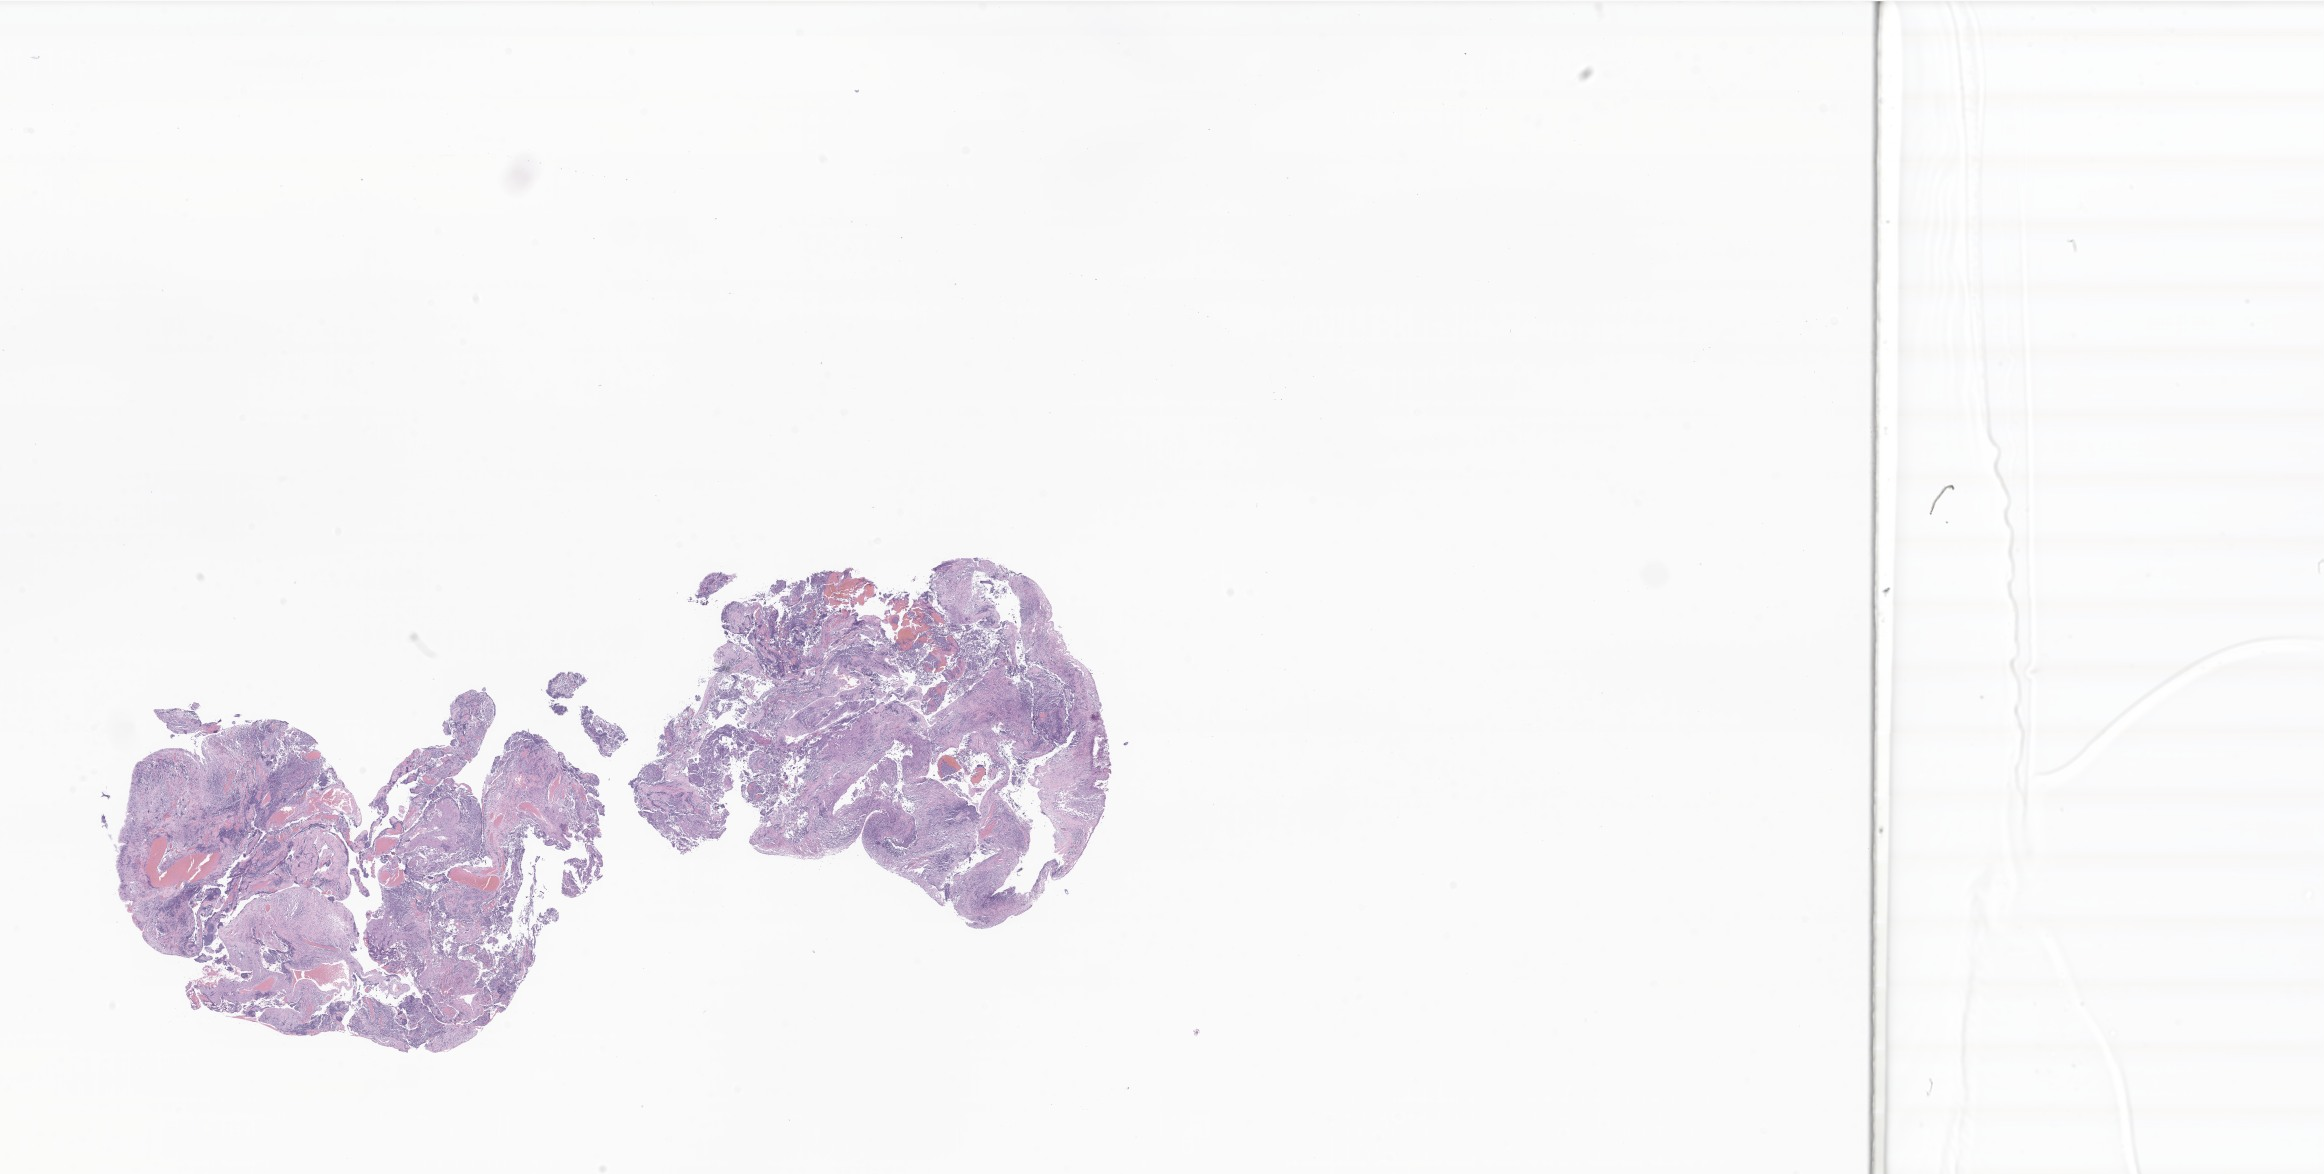
Whole-slide image, hematoxylin and eosin (H&E) stain of tumor tissue from the temporal lobe, shown as a low-resolution overview of the whole scanned area (about 39.2 x 19.8 mm). Formalin-fixed, paraffin-embedded (FFPE) tissue. Patient female; age 80 months (6 years 8 months).
• diagnosis: Choroid plexus papilloma, NOS